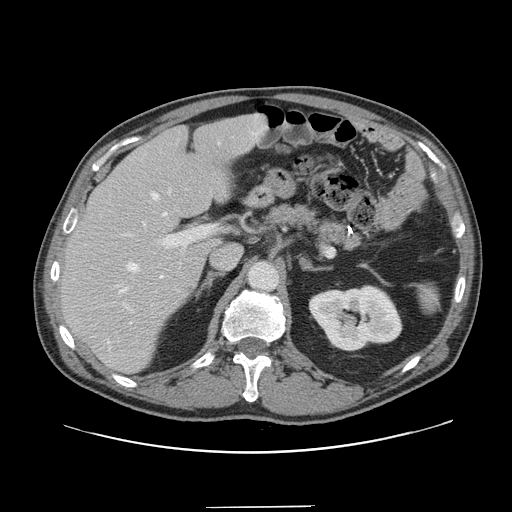
Contrast-enhanced abdominal CT, one axial slice. Slice 90 of 139 in the series (ordered by position). 120 kVp. Intravenous contrast given. Soft-tissue window (W 400 / L 40 HU). 2.5 mm slice thickness. 512 × 512 image matrix, field of view 397 × 397 mm. Male patient, age 64 years. Case-level facts recorded for this patient, not image findings: diagnosis: colorectal cancer liver metastases, imaged before liver resection; multiple liver metastases: yes; largest metastasis: 3.5 cm; chemotherapy before resection: yes.
Annotated regions visible in this slice (outlined manually by an expert reader):
- hepatic veins: box from (x=120, y=133) to (x=258, y=324) px
- liver: (x=62, y=115)–(x=265, y=372)
- planned liver remnant (the part of the liver to remain after resection): (x=62, y=115)–(x=266, y=372)
- portal vein (with intrahepatic branches): (x=121, y=225)–(x=217, y=310)